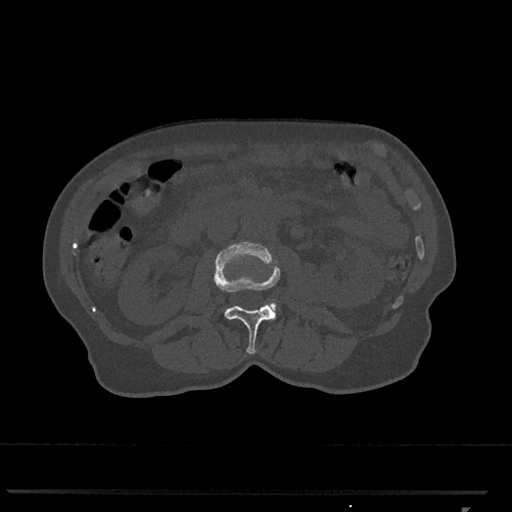
CT including the spine, one axial slice. Slice 320 of 793 in the series (ordered by position). Bone window (W 1800 / L 400 HU). 0.5 mm slice thickness. 512 × 512 image matrix. Female patient, age 62 years. Case-level facts recorded for this patient, not image findings: primary cancer: renal.
Outlined on this slice (semi-automatic segmentation, software-assisted and operator-edited):
- L2 vertebra: bounding box [x1, y1, x2, y2] px = [214, 242, 281, 354]
- L3 vertebra: [269, 303, 277, 308]